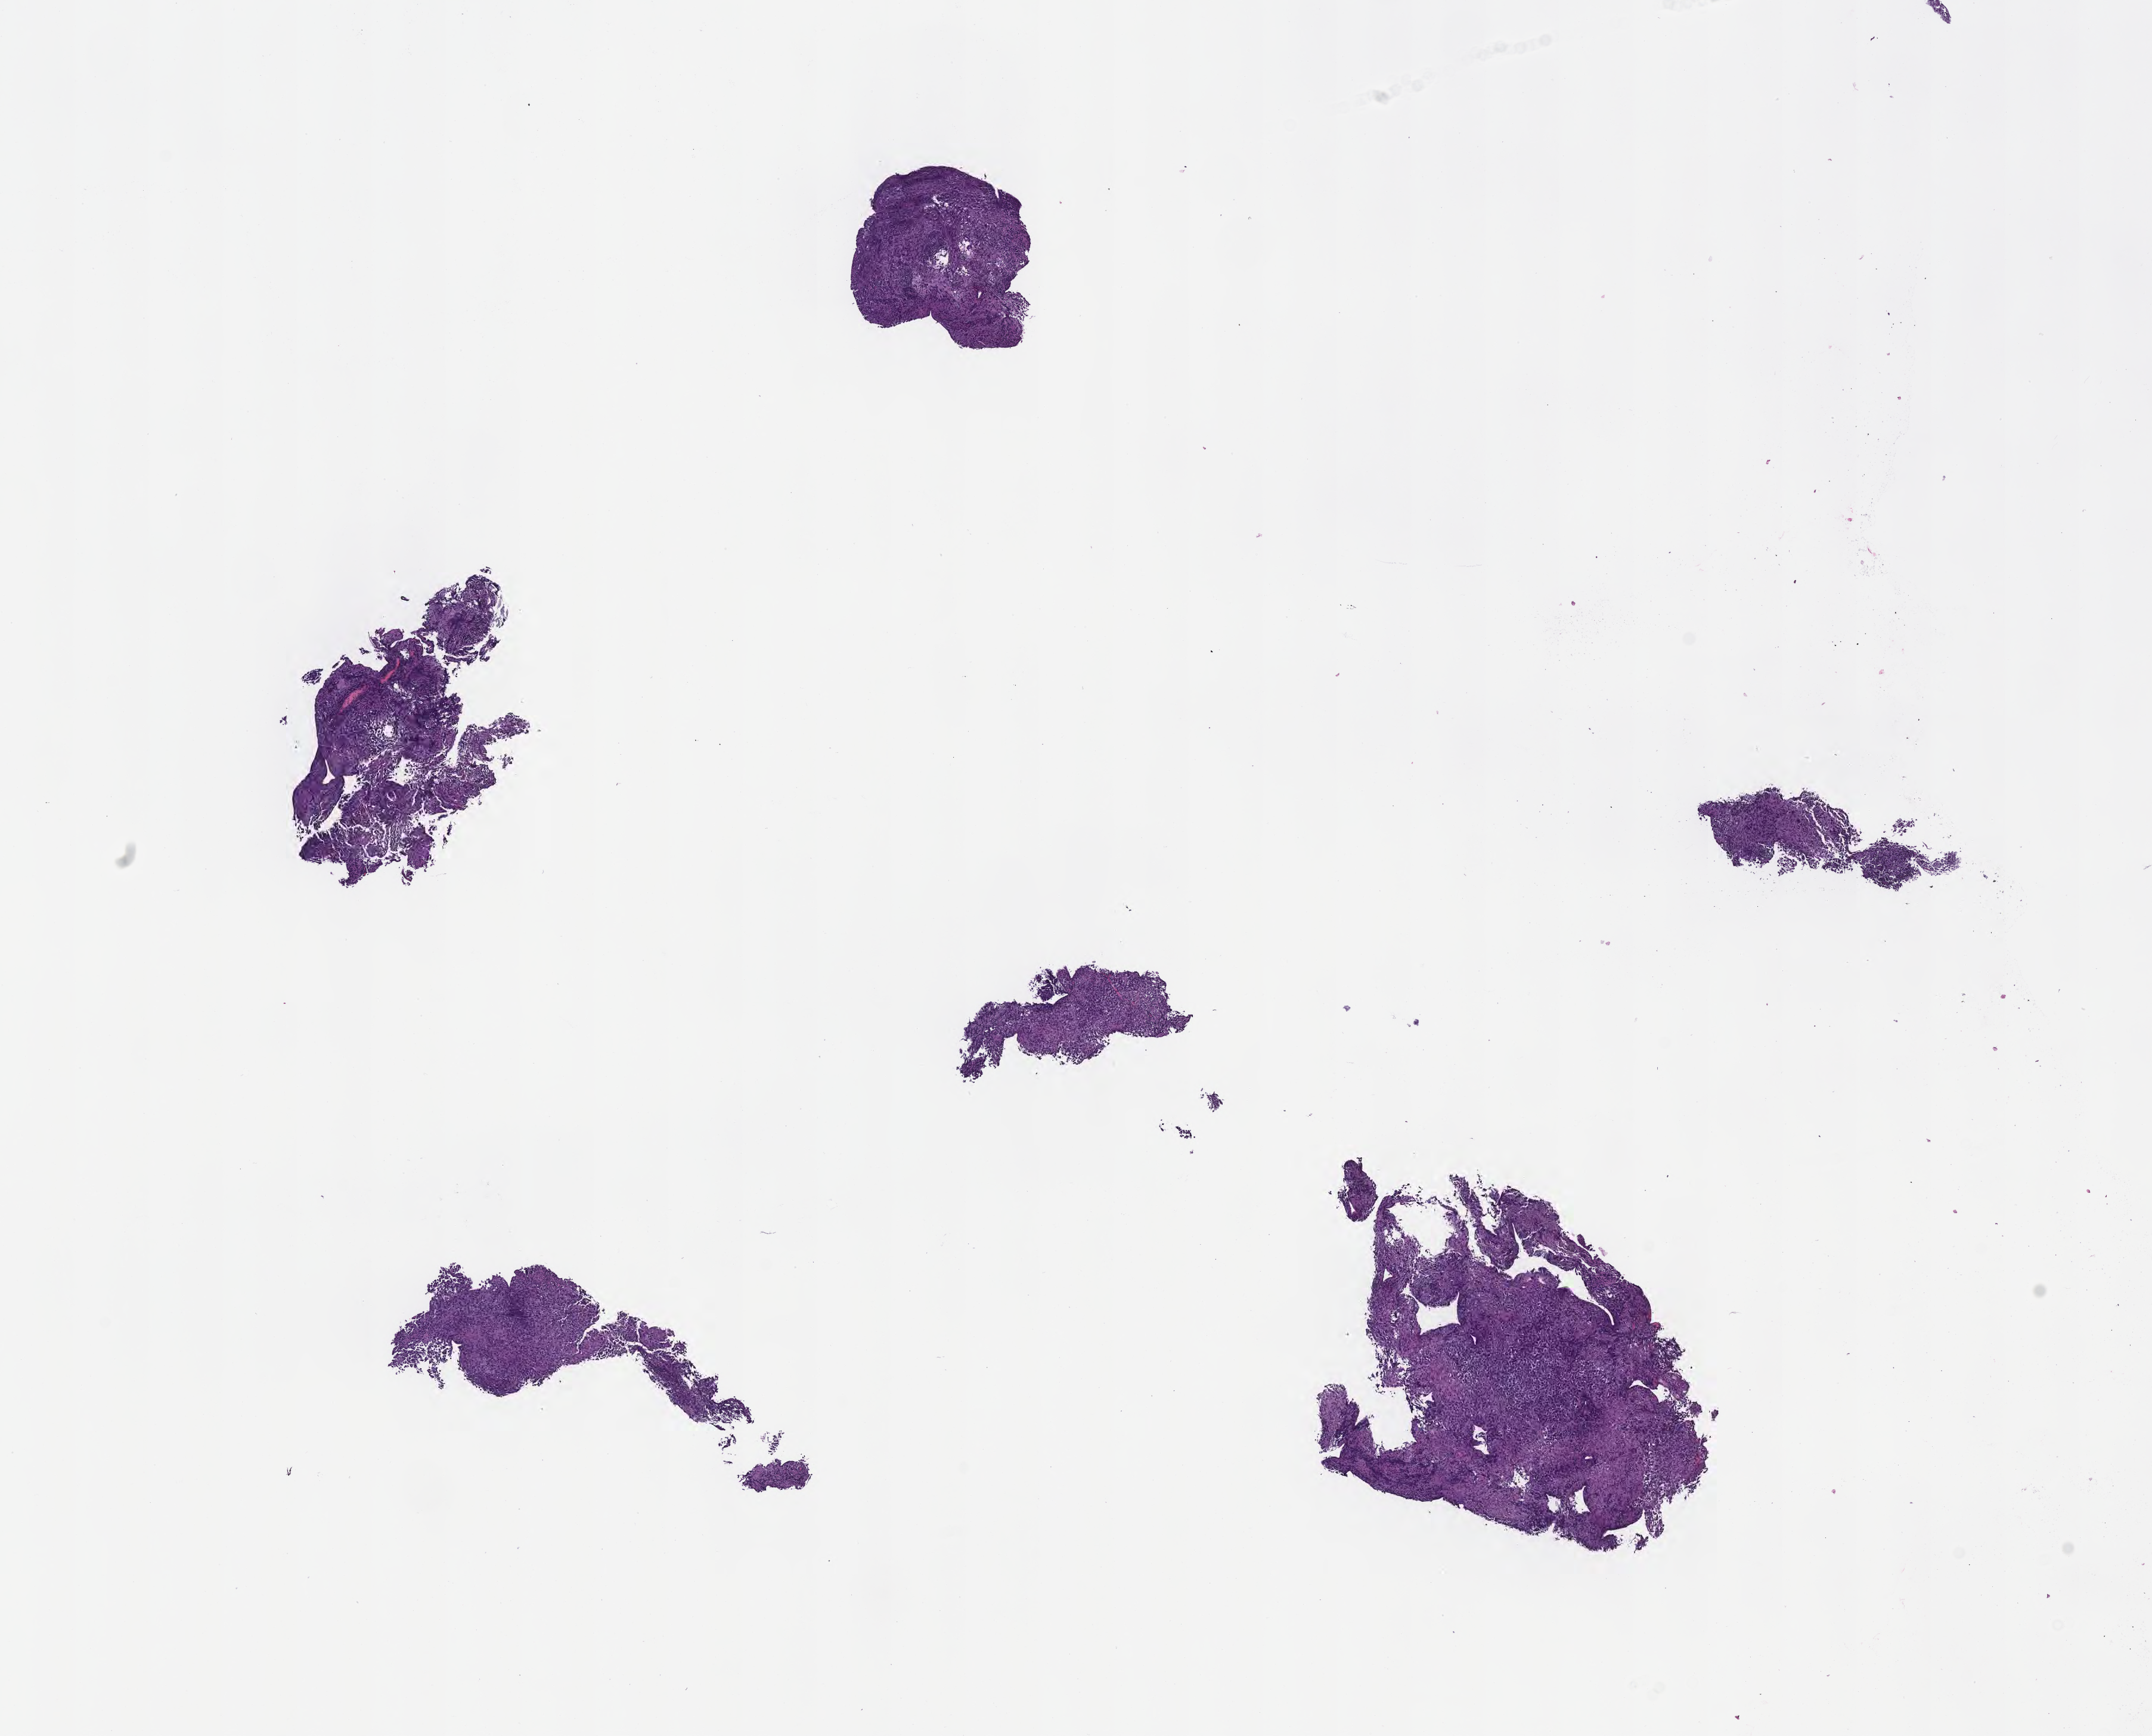
H&E whole-slide image of tumor tissue from the brain — low-resolution overview of the scanned area, about 14.6 x 11.8 mm, formalin-fixed, paraffin-embedded (FFPE) tissue. Male patient, age 194 months (16 years 2 months).
Diagnosis: Germinoma.